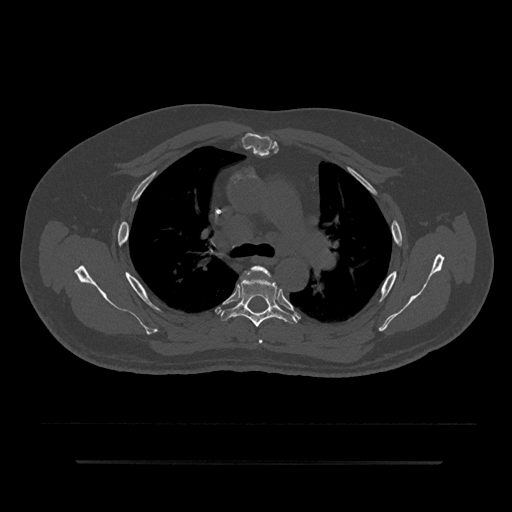
CT including the spine, one axial slice; slice 581 of 797 in the series (ordered by position); bone window (W 1800 / L 400 HU); 512 × 512 image matrix. Patient: male, 59 years. From the clinical record (not read from this slice): primary cancer: bile ducts; vertebrae with lytic lesions (as recorded): T10.
Structures marked on this image (semi-automatically segmented with operator editing):
- T4 vertebra: bounding box <252,265,270,344> (left, top, right, bottom; pixels)
- T5 vertebra: <221,277,298,327>